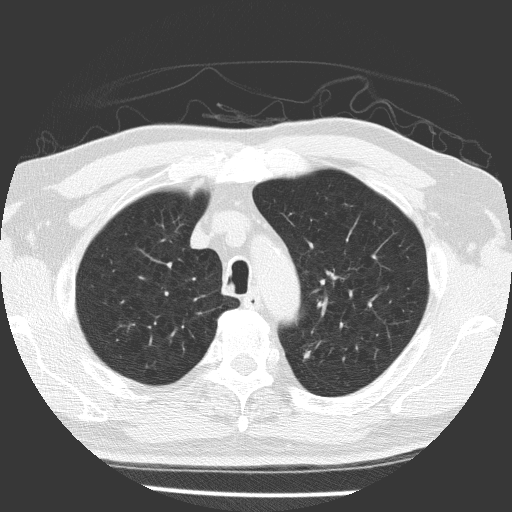
Axial slice from a low-dose chest CT screening exam, baseline annual screen, lung window (W 1500 / L -600 HU), 2 mm slice thickness, lung (sharp) reconstruction kernel (FC51), 120 kVp, slice 39 of 169 in the series. Male, age 64 years at enrolment. Former smoker at enrolment.
Expert-annotated lung lesion, box from (x=288, y=337) to (x=324, y=374) px. Reader record for this screening exam (exam-level; its link to the box is not recorded): non-calcified nodule or mass ≥4 mm, left upper lobe, 9 × 7 mm, spiculated (stellate) margins, soft tissue attenuation. Official screen result: positive, change unspecified: nodule(s) >= 4 mm or enlarging nodule(s), mass(es), or other non-specific abnormalities suspicious for lung cancer. Lung cancer was diagnosed 70 days after this screen: adenocarcinoma, NOS, left upper lobe, poorly differentiated (G3), stage IIA (AJCC 6th edition), 9 mm at pathology.